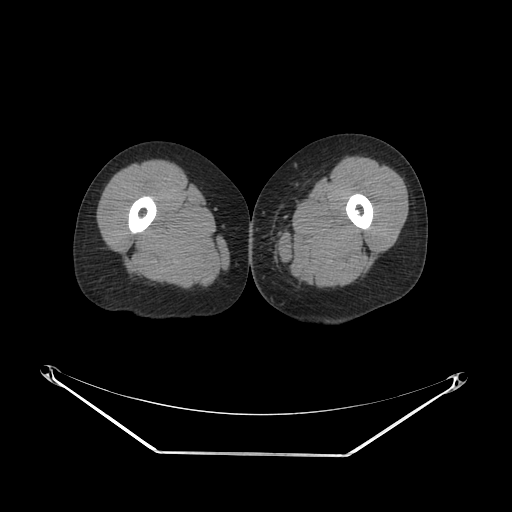
CT of an extremity soft-tissue mass (from a PET/CT study), one axial slice. Soft-tissue window (W 400 / L 40 HU). 3.75 mm slice thickness. 512 × 512 image matrix, field of view 500 × 500 mm. Female patient. From the clinical record (not read from this slice): histological type: leiomyosarcoma; grade: high; site of the primary tumour: groin.
Annotated regions visible in this slice (expert contour drawn on MRI and transferred to this co-registered scan by the dataset authors):
- gross tumour volume including surrounding oedema: box from (x=249, y=235) to (x=277, y=247) px